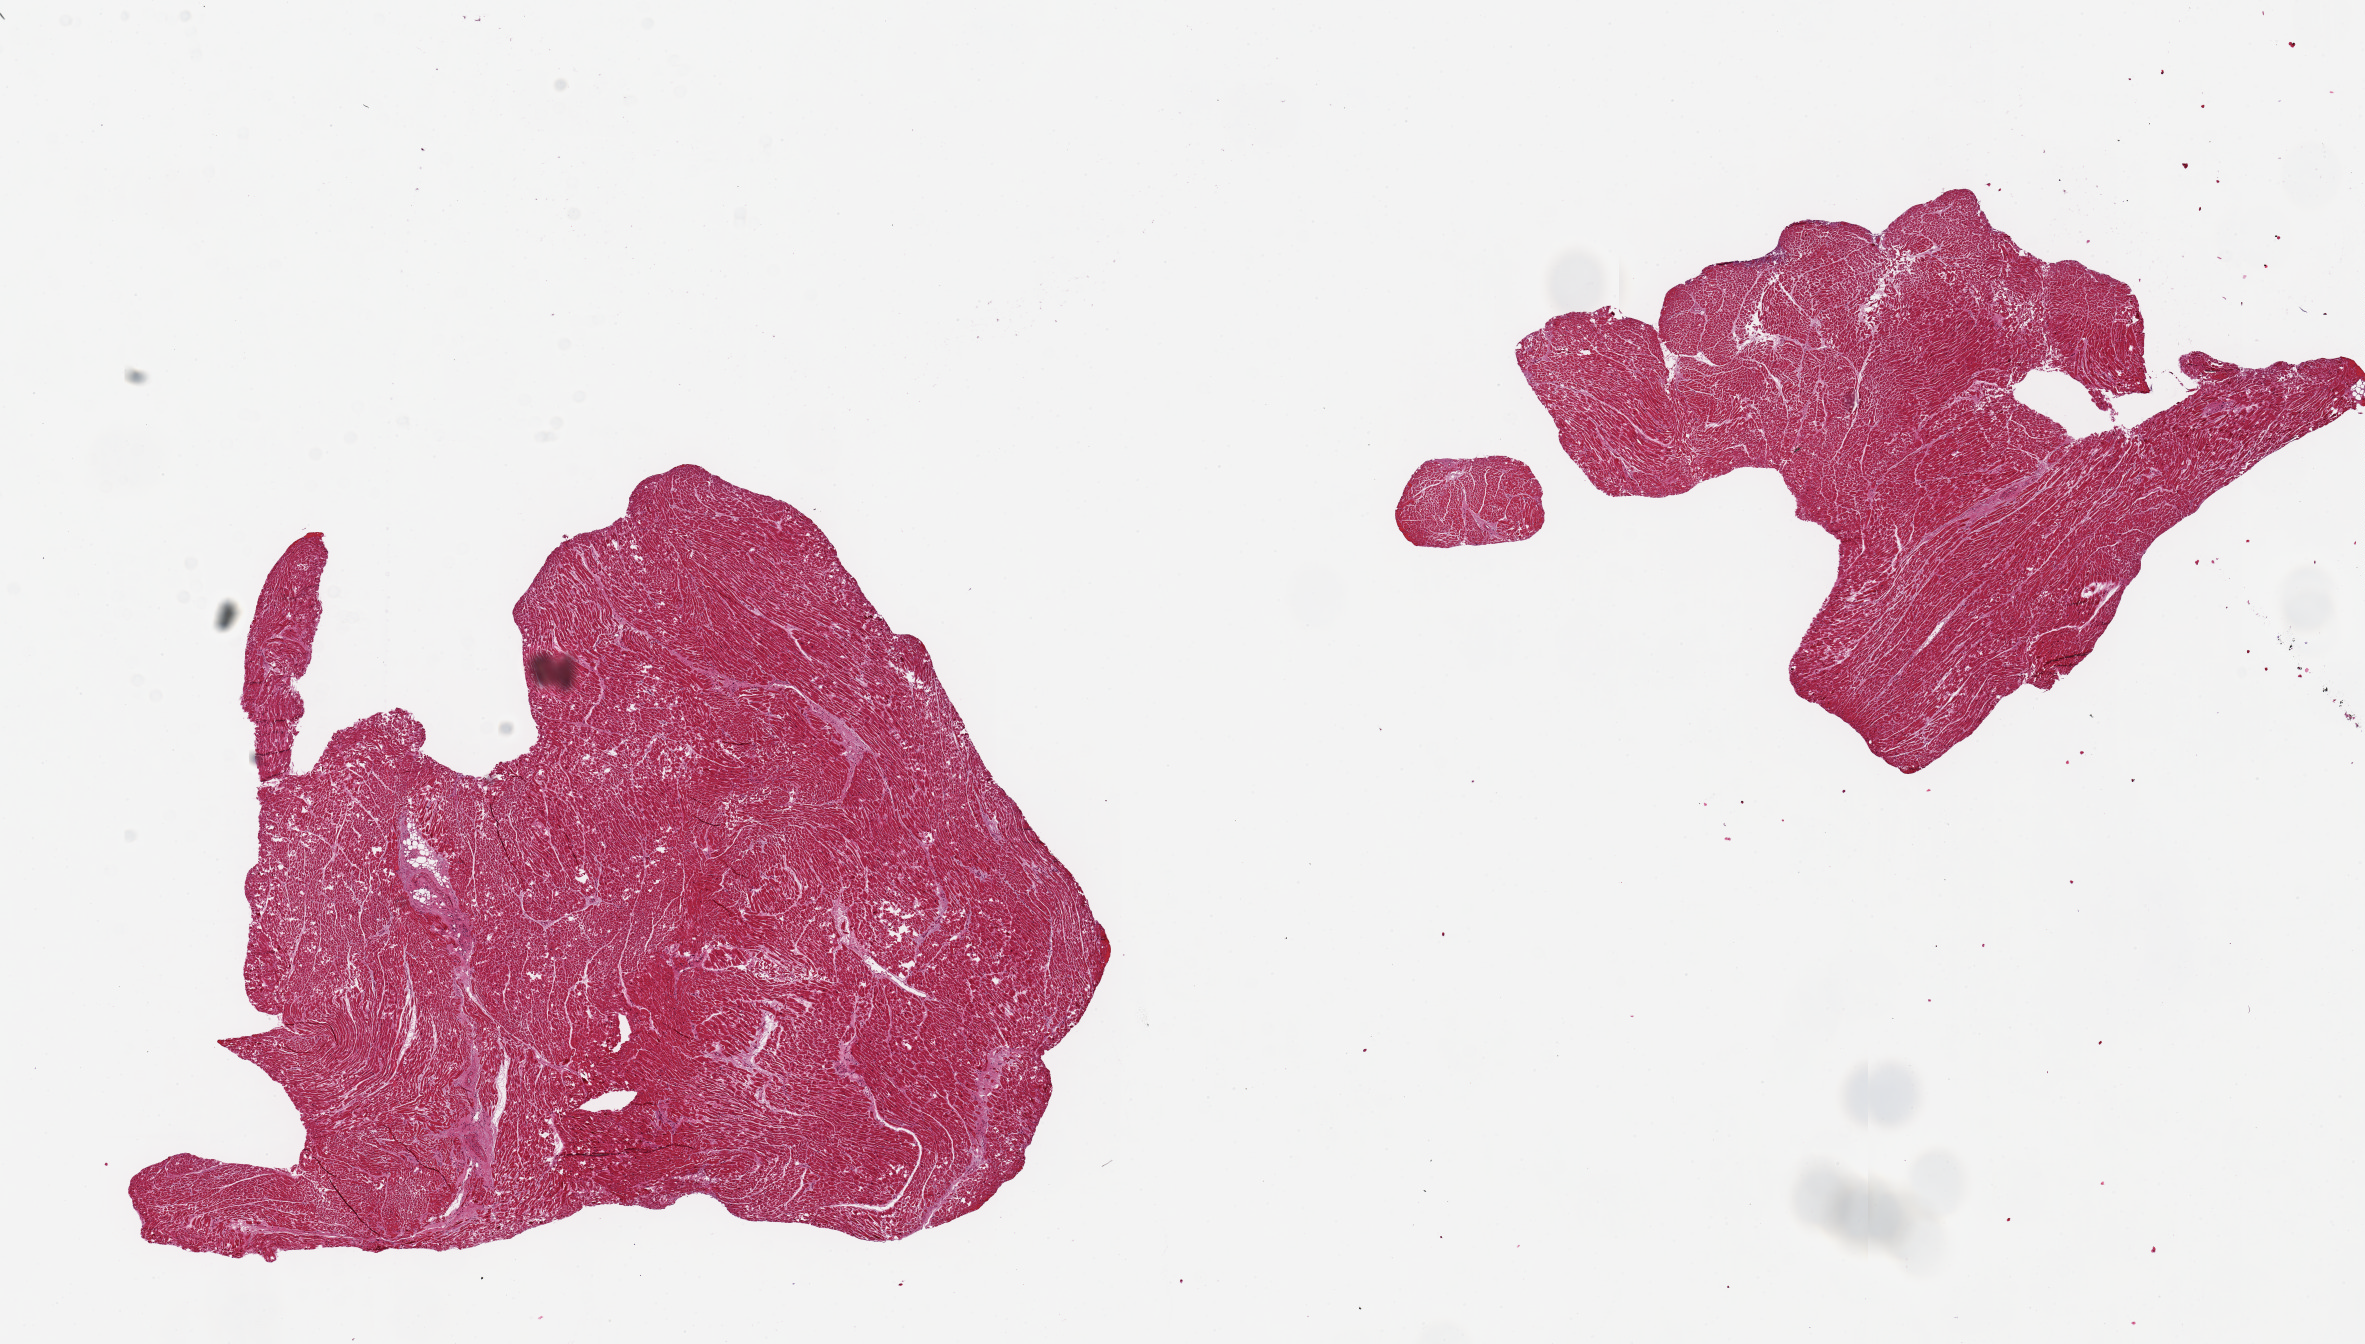
Whole-slide image, haematoxylin and eosin stain, shown as a low-resolution overview of the whole scanned area (about 18.7 x 10.6 mm, from a 20x scan). PAXgene-fixed, paraffin-embedded tissue. Section of heart (target tissue). Tissue donor sample. Donor: male.
Reviewer comment on this tissue sample: 2 pieces, 8x6 & 5x5mm; no lesions.